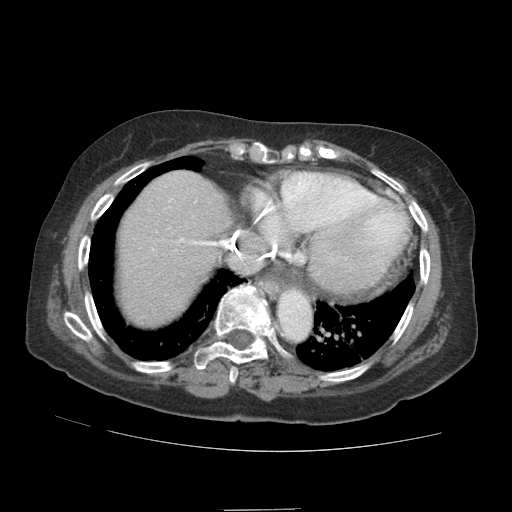
Contrast-enhanced abdominal CT (liver protocol), one axial slice. Slice 78 of 89 in the series (ordered by position). Reconstruction kernel STANDARD. 140 kVp. Soft-tissue window (W 400 / L 40 HU). 512 × 512 image matrix, field of view 360 × 360 mm. From the clinical record (not read from this slice): diagnosis: hepatocellular carcinoma (patient treated with transarterial chemoembolisation; whether this scan precedes or follows treatment is not stated here); TNM stage (as recorded): Stage-II; Child-Pugh class: A; tumour differentiation: moderately differentiated; tumour nodularity: multinodular.
Annotated regions visible in this slice (semi-automatic segmentation, software-assisted and operator-edited):
- abdominal aorta: bounding box <278,292,310,337> (left, top, right, bottom; pixels)
- liver parenchyma outside the tumour (the mass and vessels are separate outlines, so this box may not span the whole liver): <120,170,232,324>
- liver vessels: <152,198,221,250>